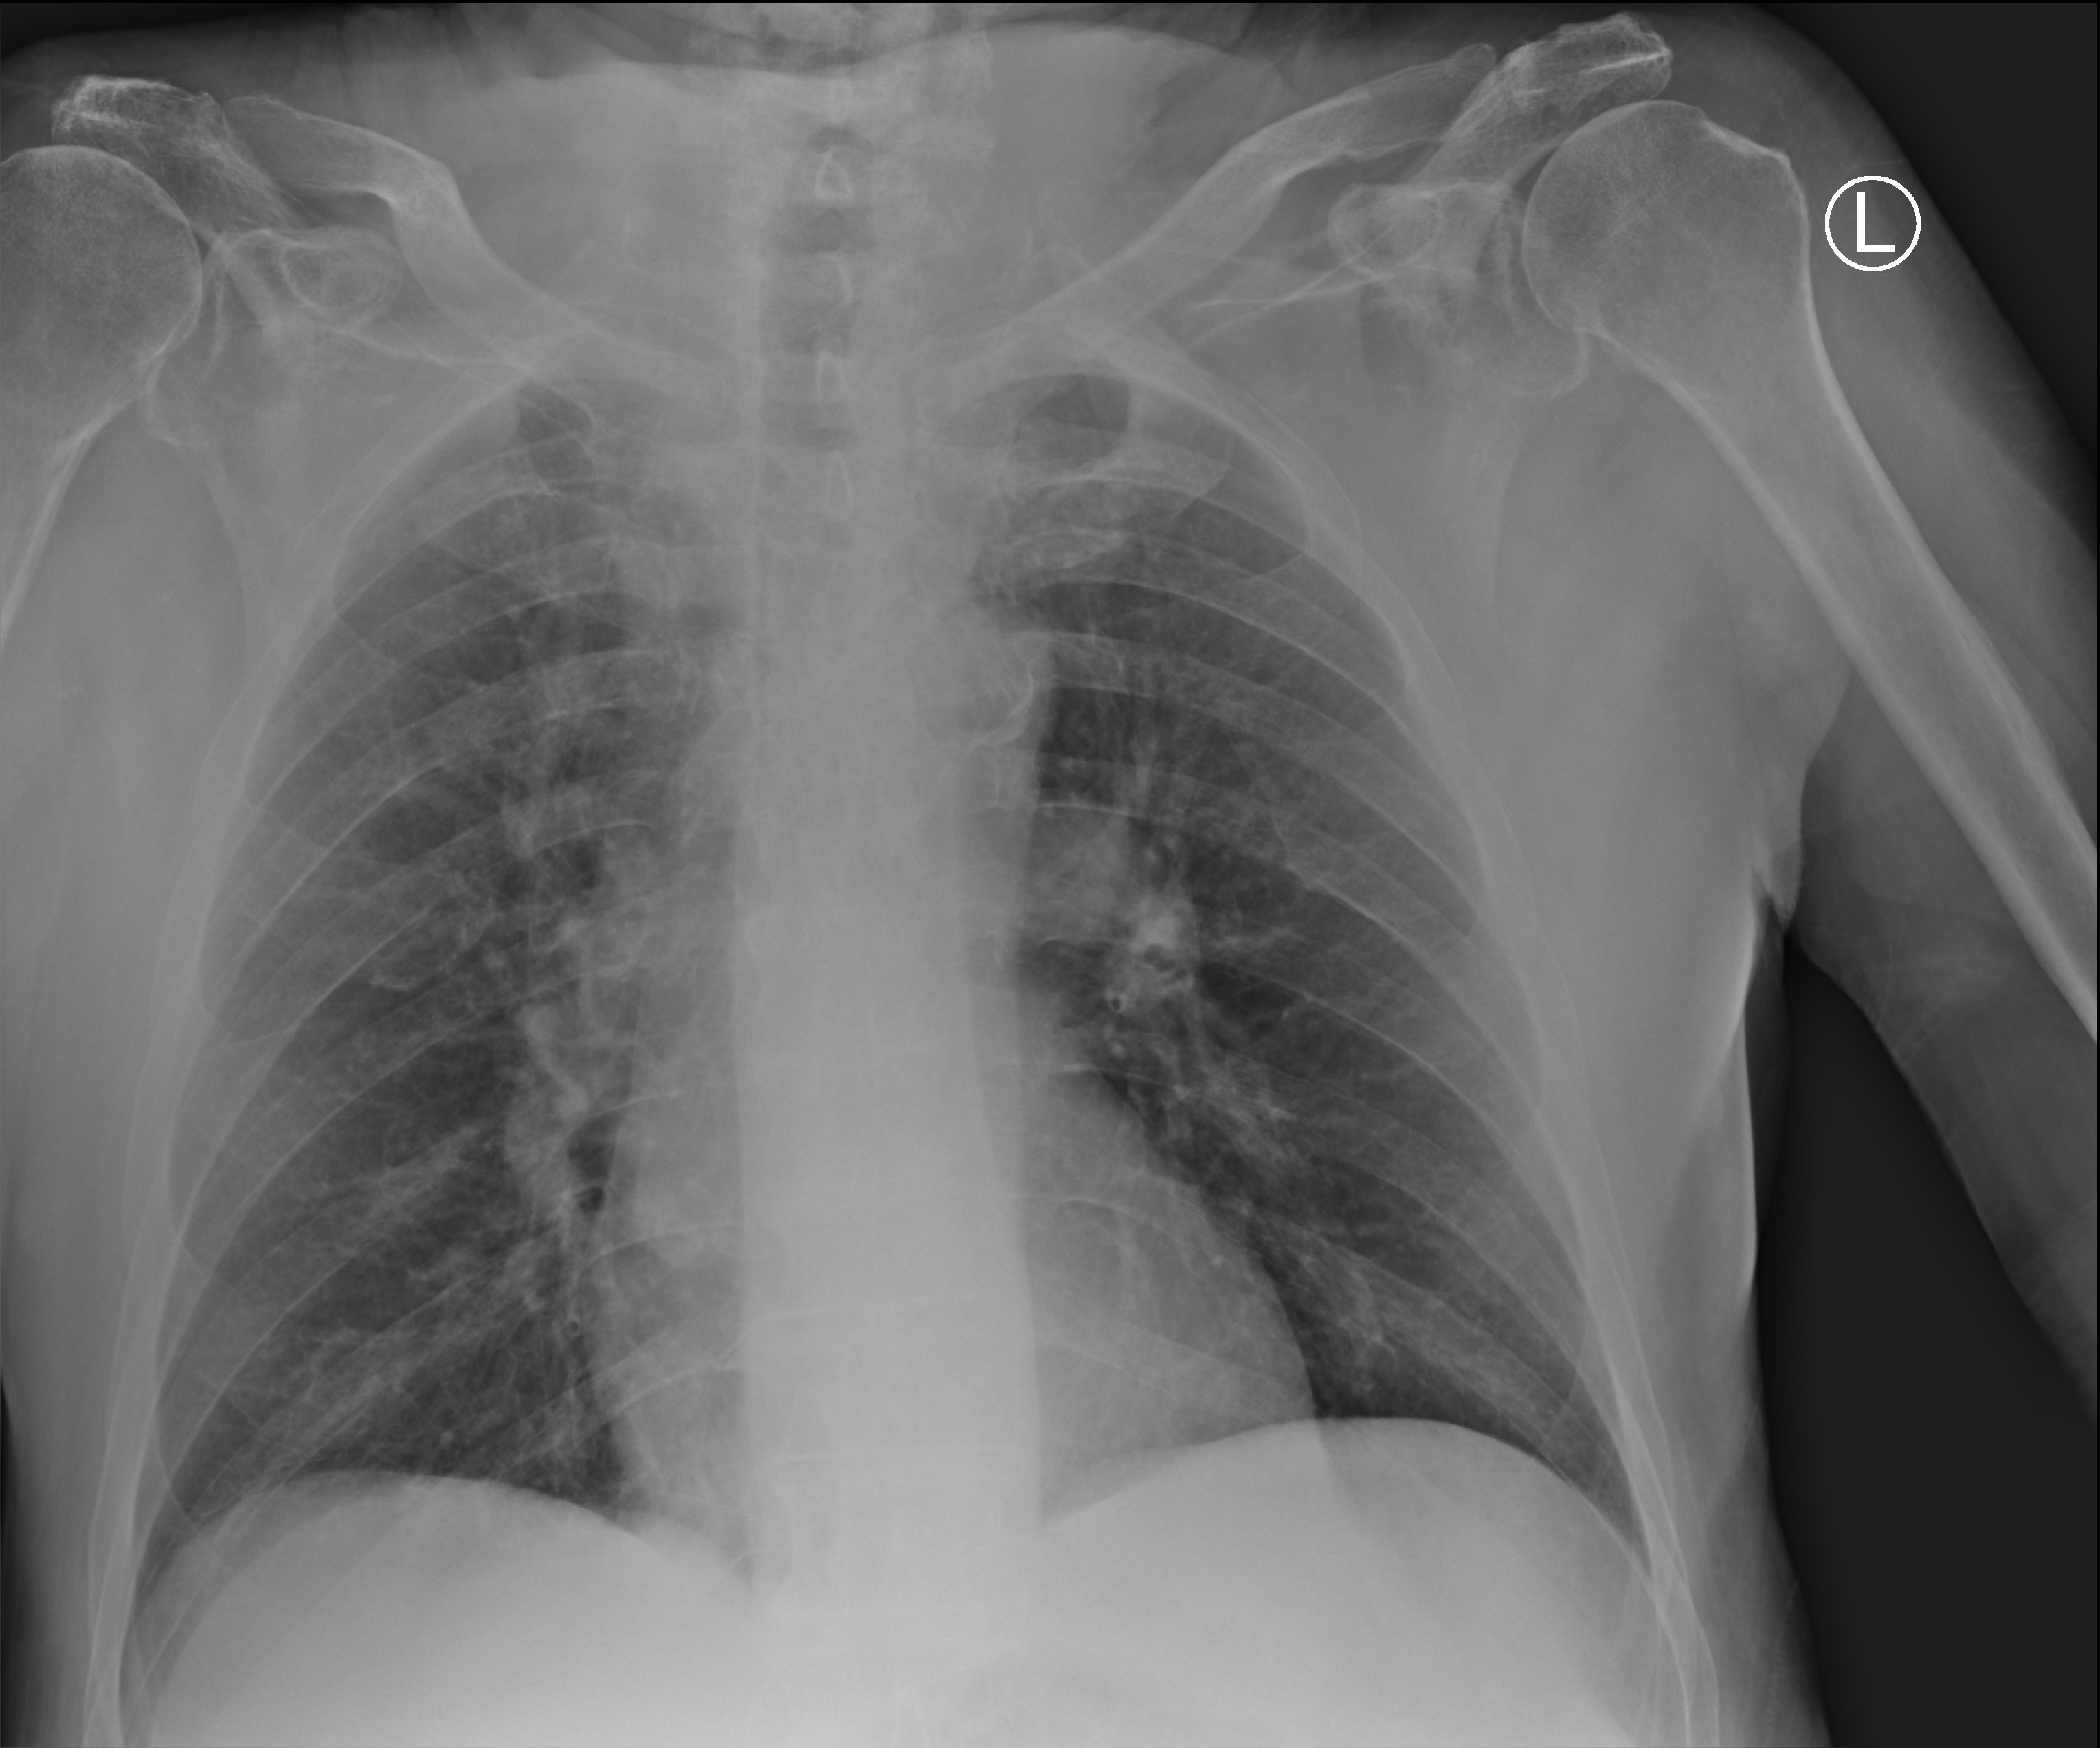
Chest X-ray (portable), anteroposterior (AP) projection. Patient hospitalised with COVID-19; male, aged 75–90 years.
Admission-level facts for this patient (not findings on this image; timing relative to this image not recorded): mechanically ventilated during this hospital stay: no; admitted to intensive care during this hospital stay: no; length of hospital stay: 5 days.